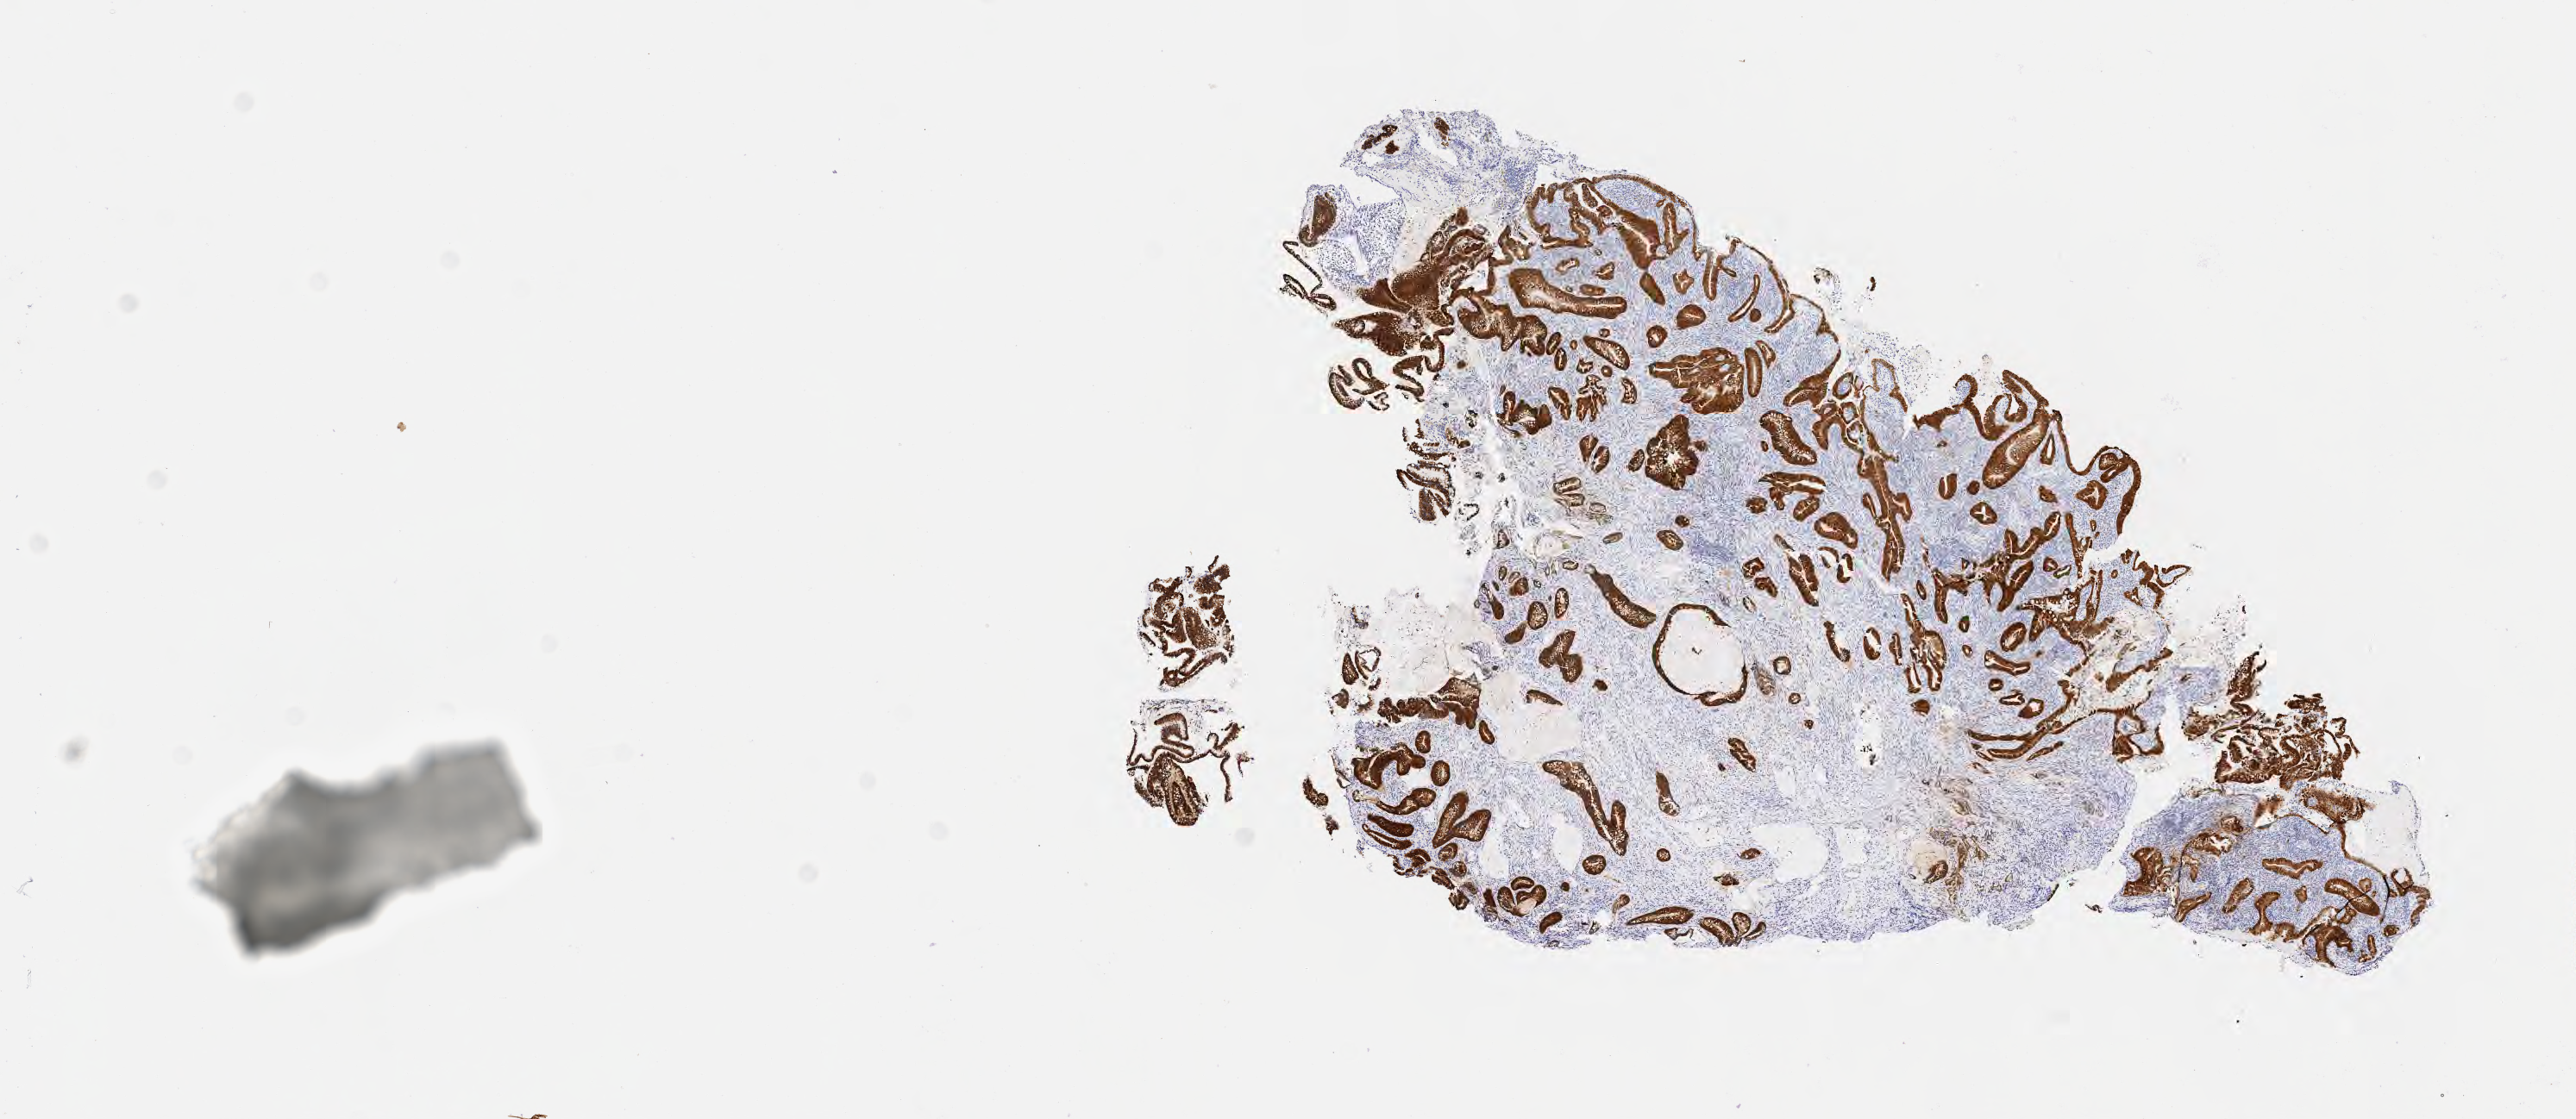
IHC for p16 (p16INK4a), whole-slide image, whole scanned area (about 12.1 x 5.2 mm) shown as a low-resolution overview; specimen: tumor tissue; anatomic site: cervix. Patient female; aged 36.
Histologic diagnosis: Adenocarcinoma, NOS.